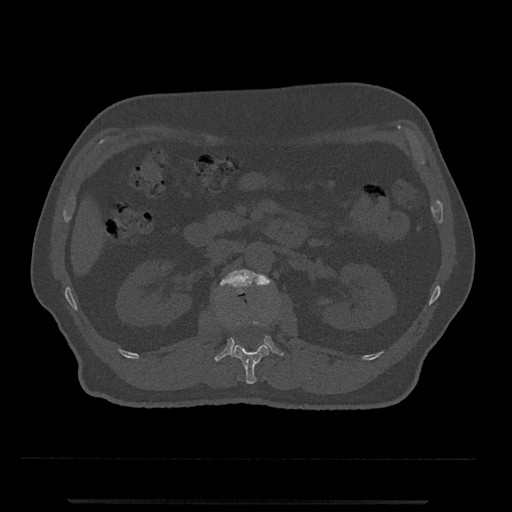
CT including the spine, one axial slice. Slice 304 of 797 in the series (ordered by position). Reconstruction kernel Br40s/3. 120 kVp. Bone window (W 1800 / L 400 HU). 512 × 512 image matrix. Patient: male, 63 years. Case-level facts recorded for this patient, not image findings: primary cancer: prostate.
Annotated regions visible in this slice (semi-automatic segmentation, software-assisted and operator-edited):
- L1 vertebra: bounding box [x1, y1, x2, y2] px = [232, 319, 272, 384]
- L2 vertebra: [214, 269, 284, 361]